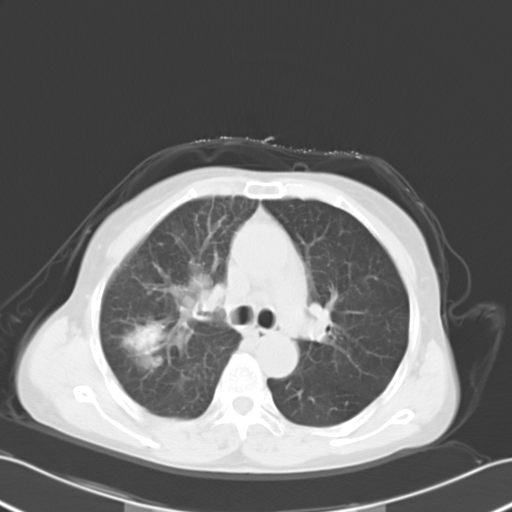
Chest CT, one axial slice; 120 kVp; lung window (W 1500 / L -600 HU); 512 × 512 image matrix, field of view 353 × 353 mm. Patient: female, 67 years. From the clinical record (not read from this slice): clinical TNM (as recorded): T2a N3 M0.
Structures marked on this image (rectangle marked by the reading radiologist):
- lung tumour (recorded histology: small cell carcinoma): bounding box <174,266,221,324> (left, top, right, bottom; pixels)